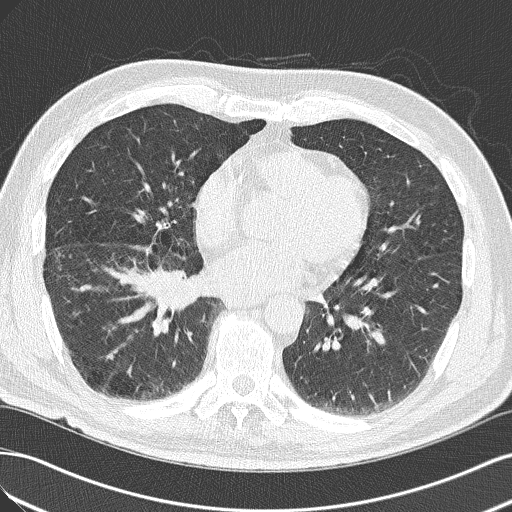
Low-dose screening chest CT, axial slice, baseline screening round, lung window (W 1500 / L -600 HU), 2 mm slice thickness, 120 kVp, slice 93 of 143 in the series. Male, age 65 years at enrolment.
Lesion marked by an expert reader, box from (x=103, y=246) to (x=203, y=339) px. Screening reader's record for this exam (one nodule recorded; not confirmed to be the boxed lesion): non-calcified nodule or mass ≥4 mm, right upper lobe, 18 × 13 mm, spiculated (stellate) margins, soft tissue attenuation. Official screen result: positive, change unspecified: nodule(s) >= 4 mm or enlarging nodule(s), mass(es), or other non-specific abnormalities suspicious for lung cancer. Later outcome: lung cancer diagnosed 14 days after this screen — adenocarcinoma, NOS, right lower lobe, poorly differentiated (G3), stage IIIA (AJCC 6th edition), 40 mm at pathology.